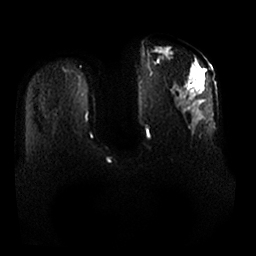
Breast MRI, one axial slice. Position 9 of 25 along the scan axis. Diffusion-weighted series; image 2 of 4 stored at this slice position (different b-values; order by instance number). 1.5 T. 256 × 256 image matrix, field of view 380 × 380 mm. Female patient.
Annotated regions visible in this slice (expert manual segmentation):
- tumour on diffusion-weighted imaging: bounding box <155,48,203,87> (left, top, right, bottom; pixels)